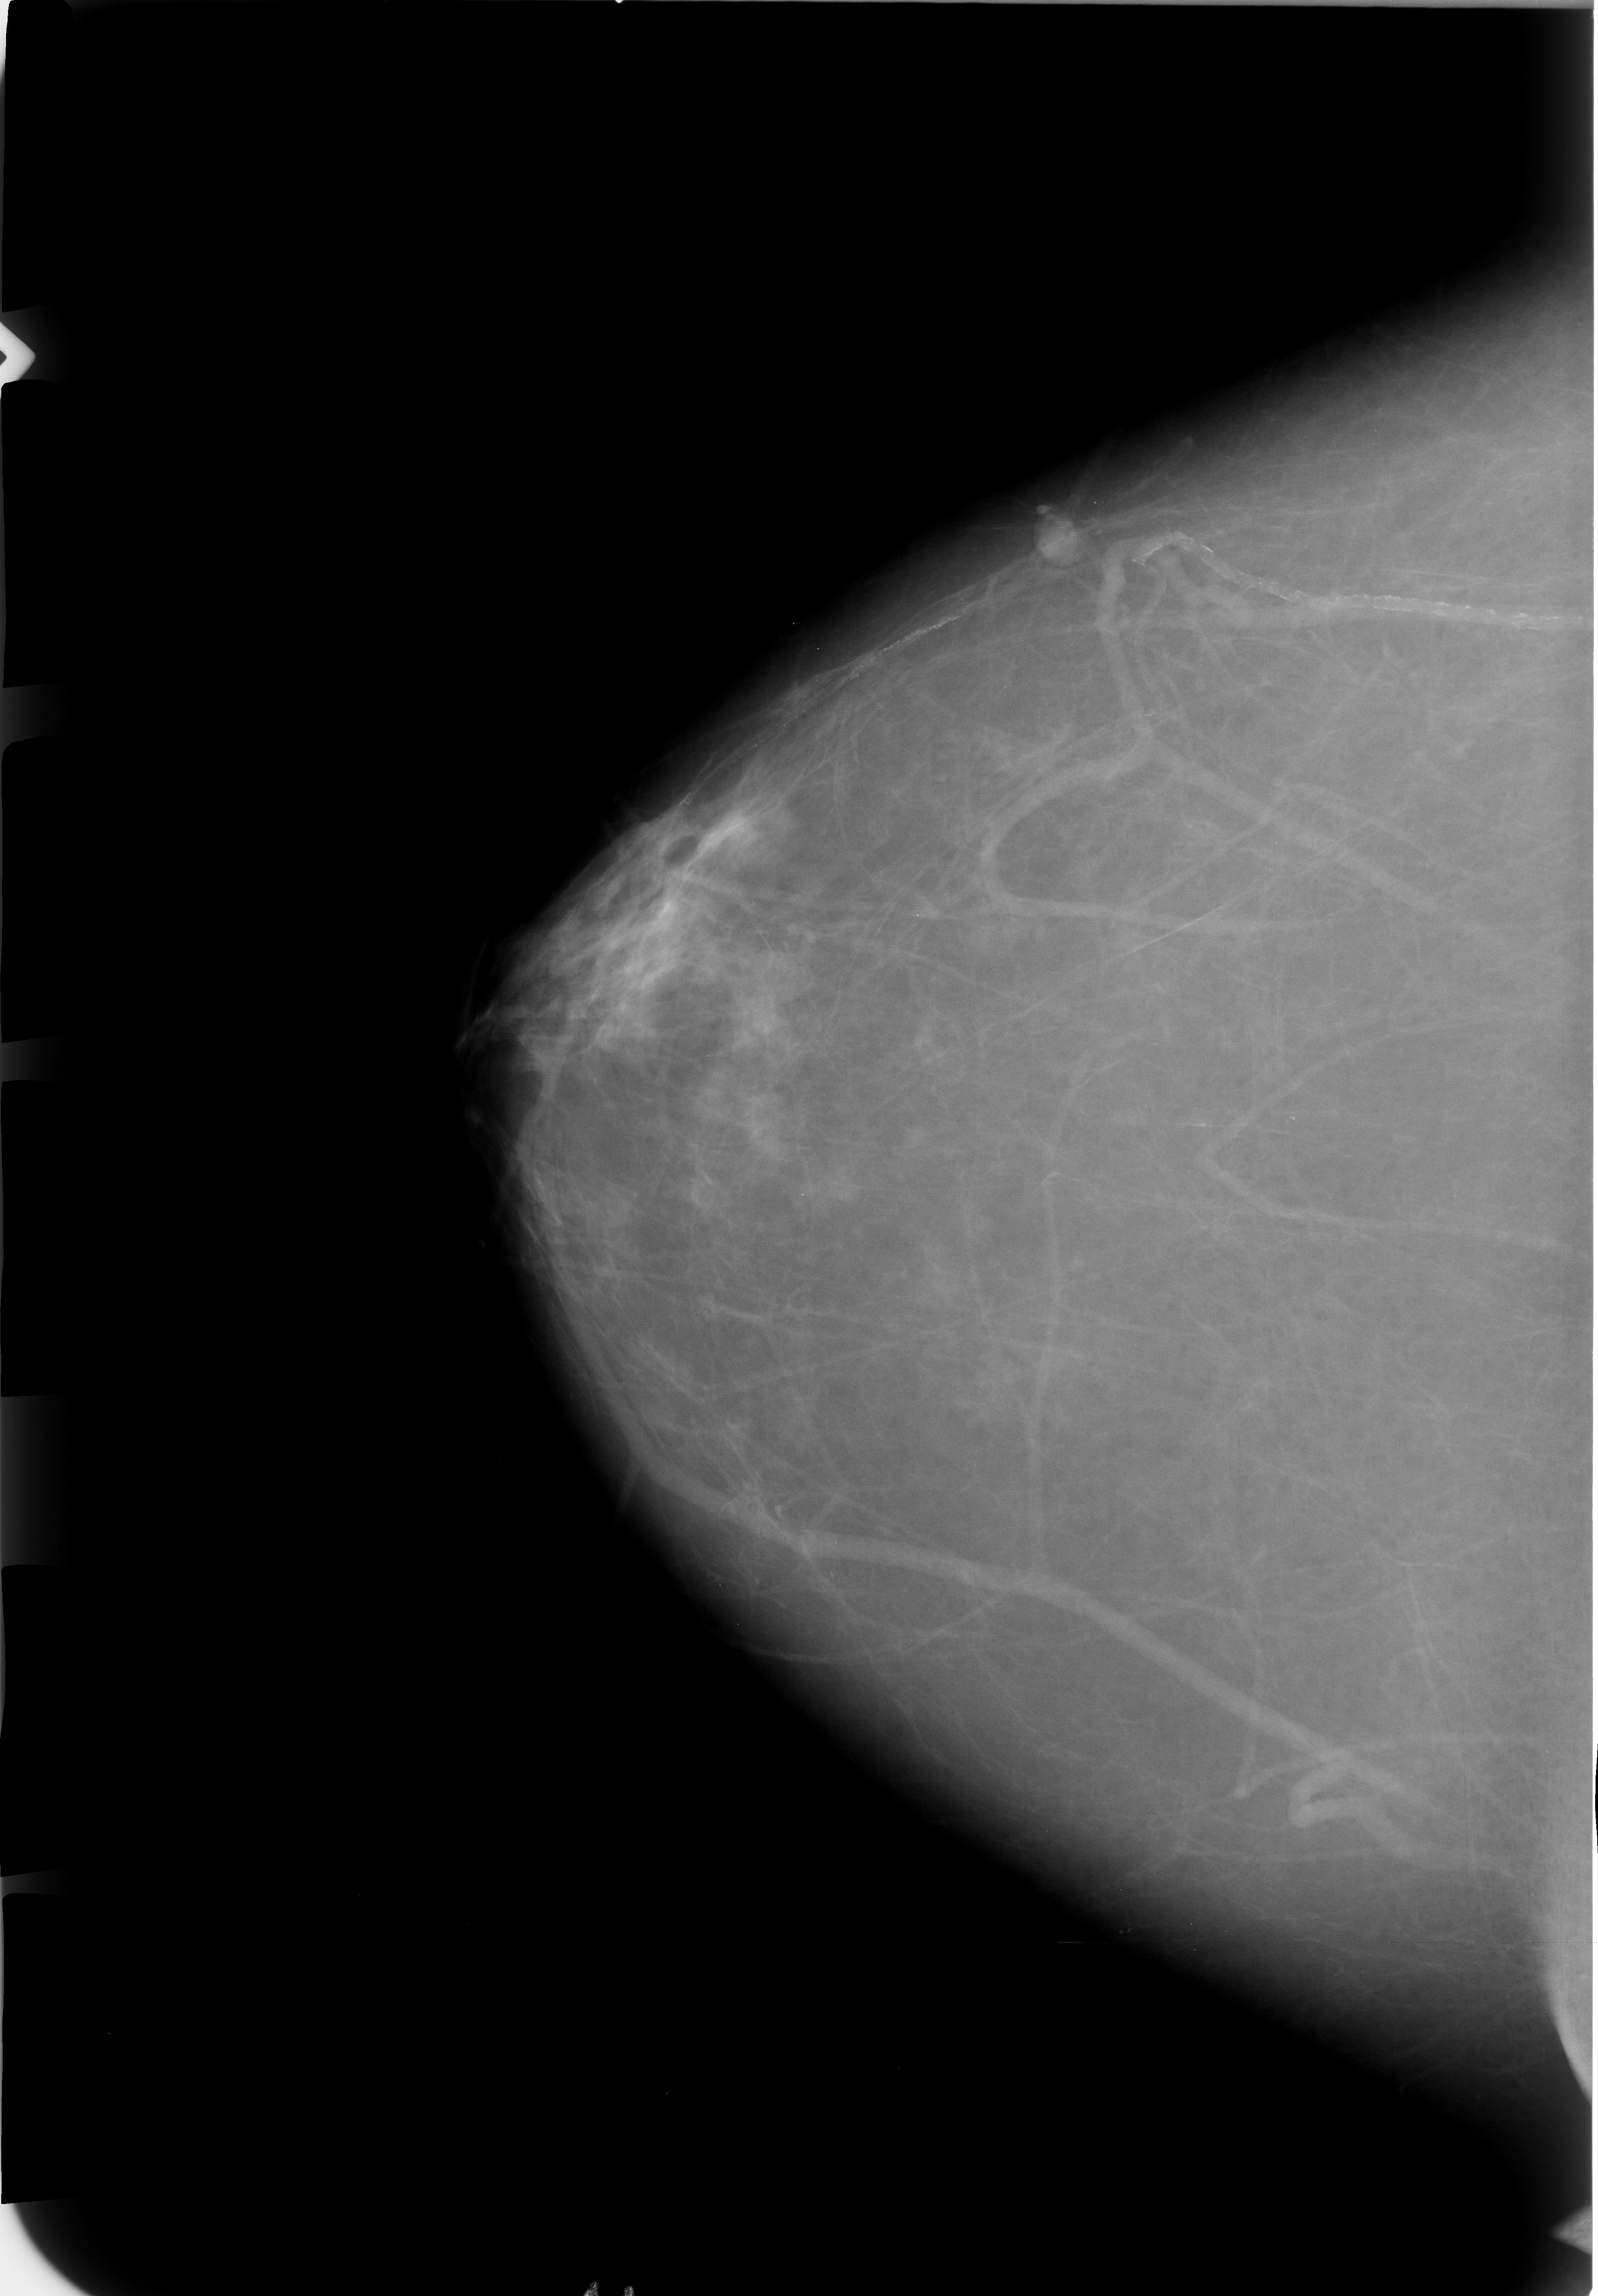
Mammogram (digitized film), right breast, craniocaudal (CC) view, breast composition: scattered fibroglandular densities (BI-RADS density category 2 of 4).
- Finding: mass, shape oval / lymph node, margins circumscribed; BI-RADS assessment category 2; subtlety rating 4 on a 1 (subtle) to 5 (obvious) scale; benign; no additional work-up was recommended (benign without callback).